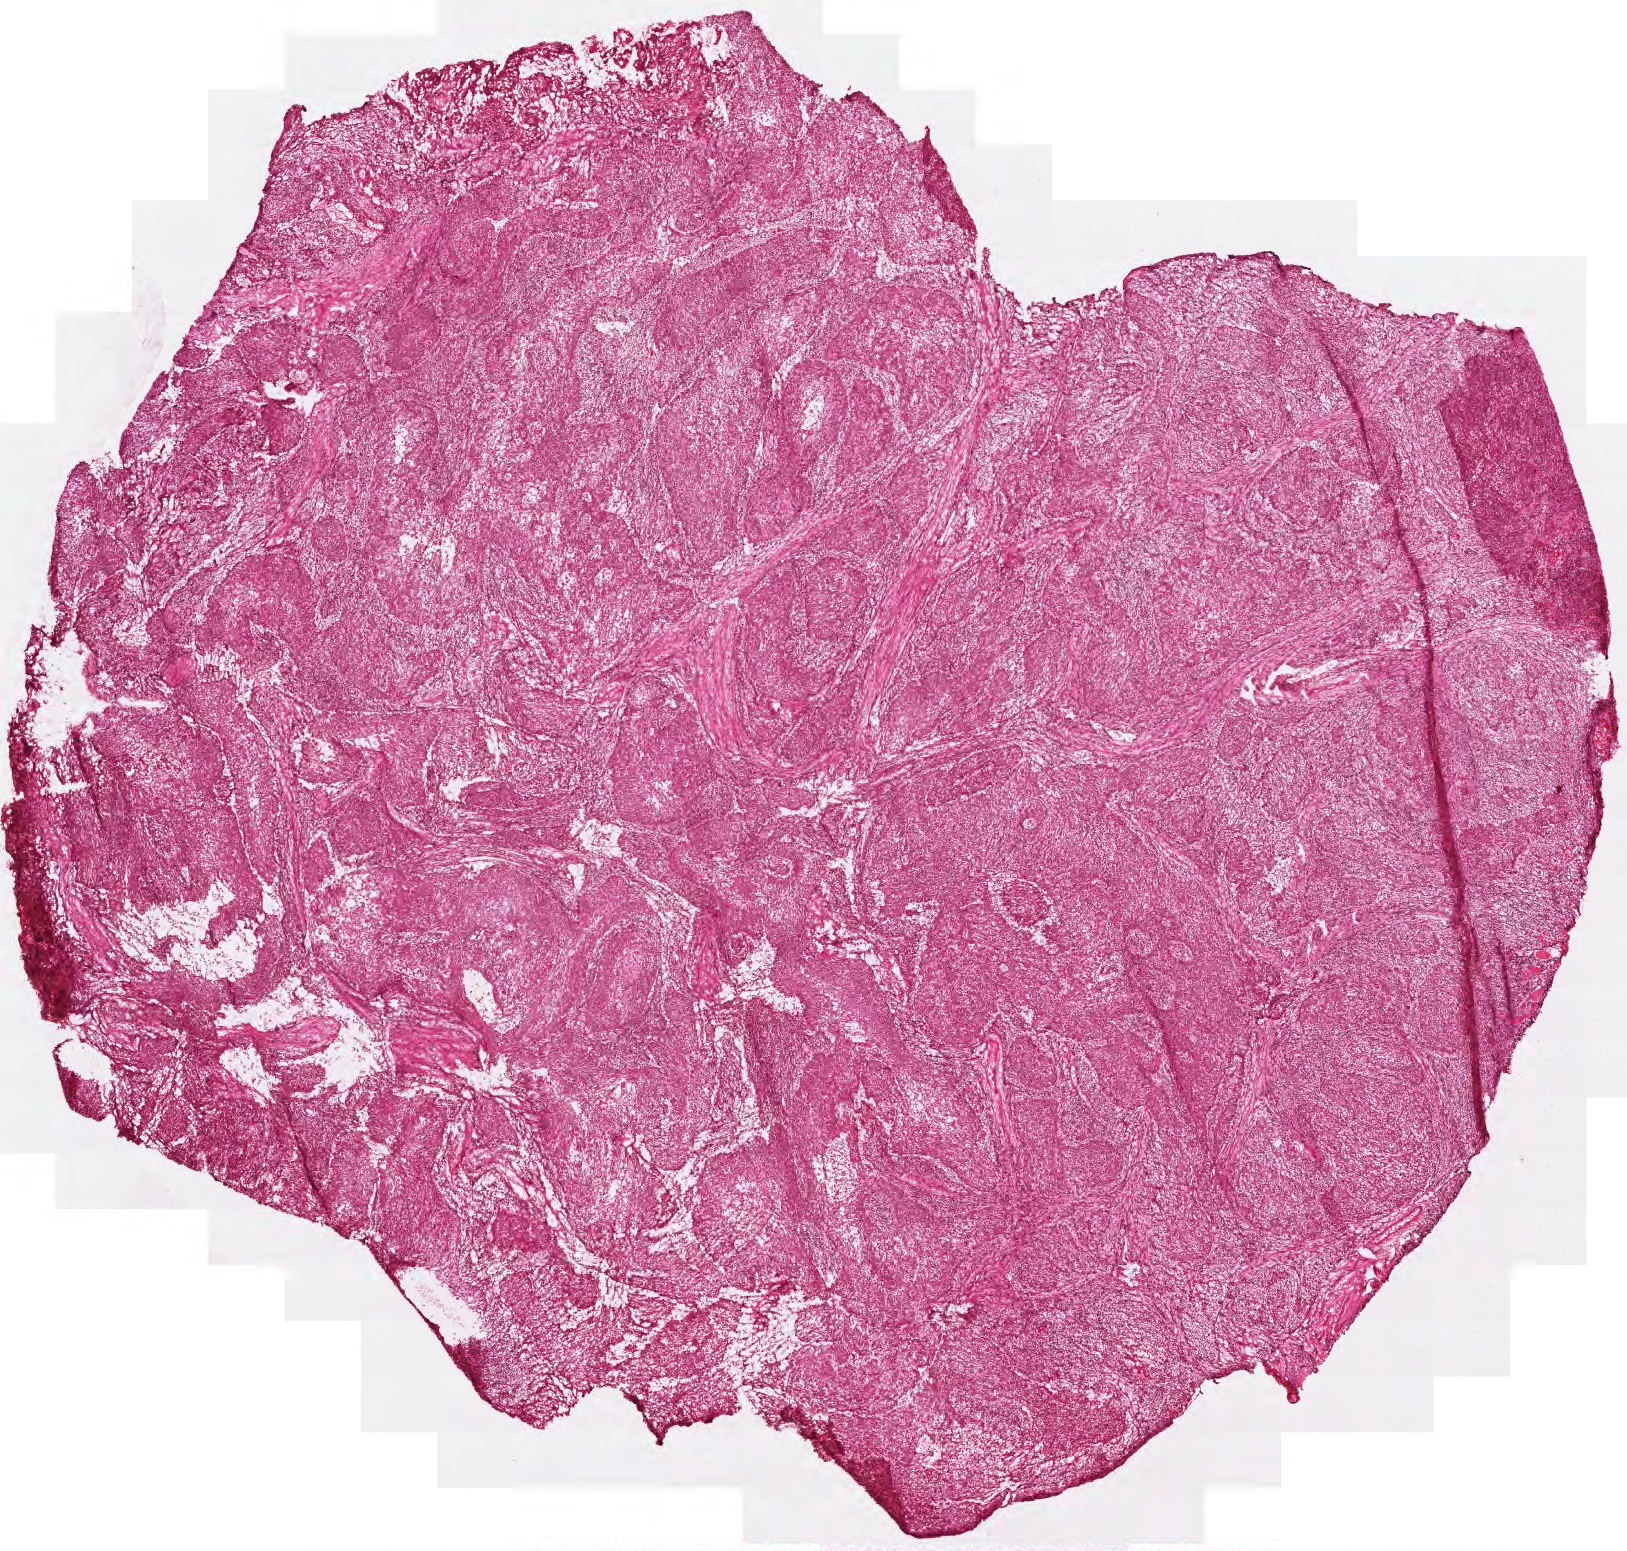
Hematoxylin and eosin (H&E) stained whole-slide image — whole scanned area (about 3.3 x 3.1 mm) shown as a low-resolution overview; frozen section from the top of the tissue portion; sample: primary tumour, head and neck. Male patient; age at initial diagnosis 50 years. Histologic grade: G3 (poorly differentiated). Pathologist review of this section (percent, as recorded): tumour cells 90%, tumour nuclei 90%, normal cells 0%, stromal cells 10%, necrosis 0%.
Histologic diagnosis: Squamous cell carcinoma, NOS (tonsil, NOS). AJCC pathologic stage: I. Laterality: left.